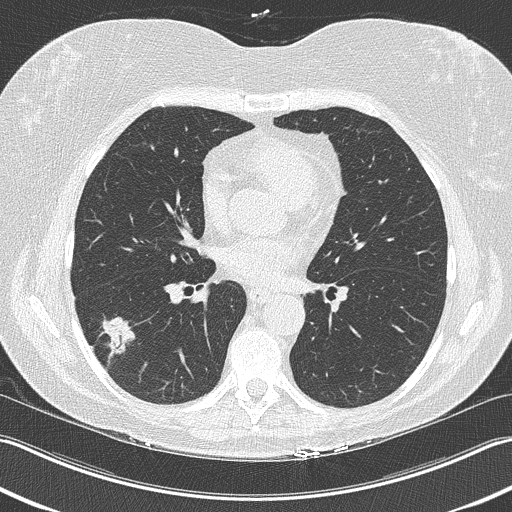
Low-dose screening chest CT, one axial slice. Position 114 of 210 along the scan axis. Reconstruction kernel B50f. 120 kVp. Lung window (W 1500 / L -600 HU). 512 × 512 image matrix, field of view 348 × 348 mm.
Annotated regions visible in this slice (expert manual segmentation):
- lesion 1 (tumor, lower lobe of right lung): bounding box [x1, y1, x2, y2] px = [99, 316, 135, 366]